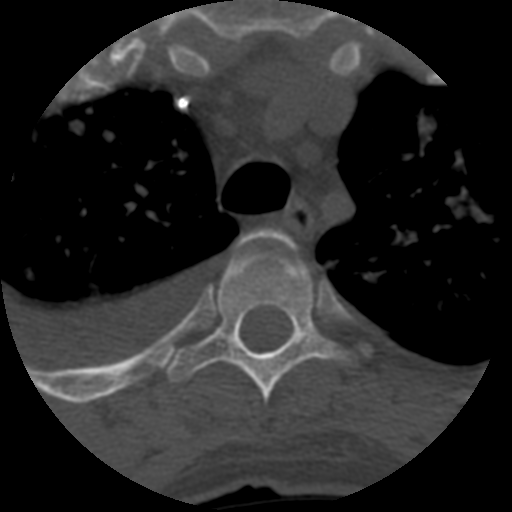
CT including the spine, one axial slice. Slice 474 of 708 in the series (ordered by position). Reconstruction kernel STANDARD. 120 kVp. One of 3 acquisitions stored at this slice position. Bone window (W 1800 / L 400 HU). 512 × 512 image matrix, field of view 160 × 160 mm. Patient age 55 years. Case-level facts recorded for this patient, not image findings: primary cancer: colon; vertebrae with lytic lesions (as recorded): T12, L1, L5.
Outlined on this slice (semi-automatic segmentation, software-assisted and operator-edited):
- T3 vertebra: bounding box (x1, y1, x2, y2) in pixels: (246, 229, 286, 242)
- T4 vertebra: (167, 238, 341, 404)